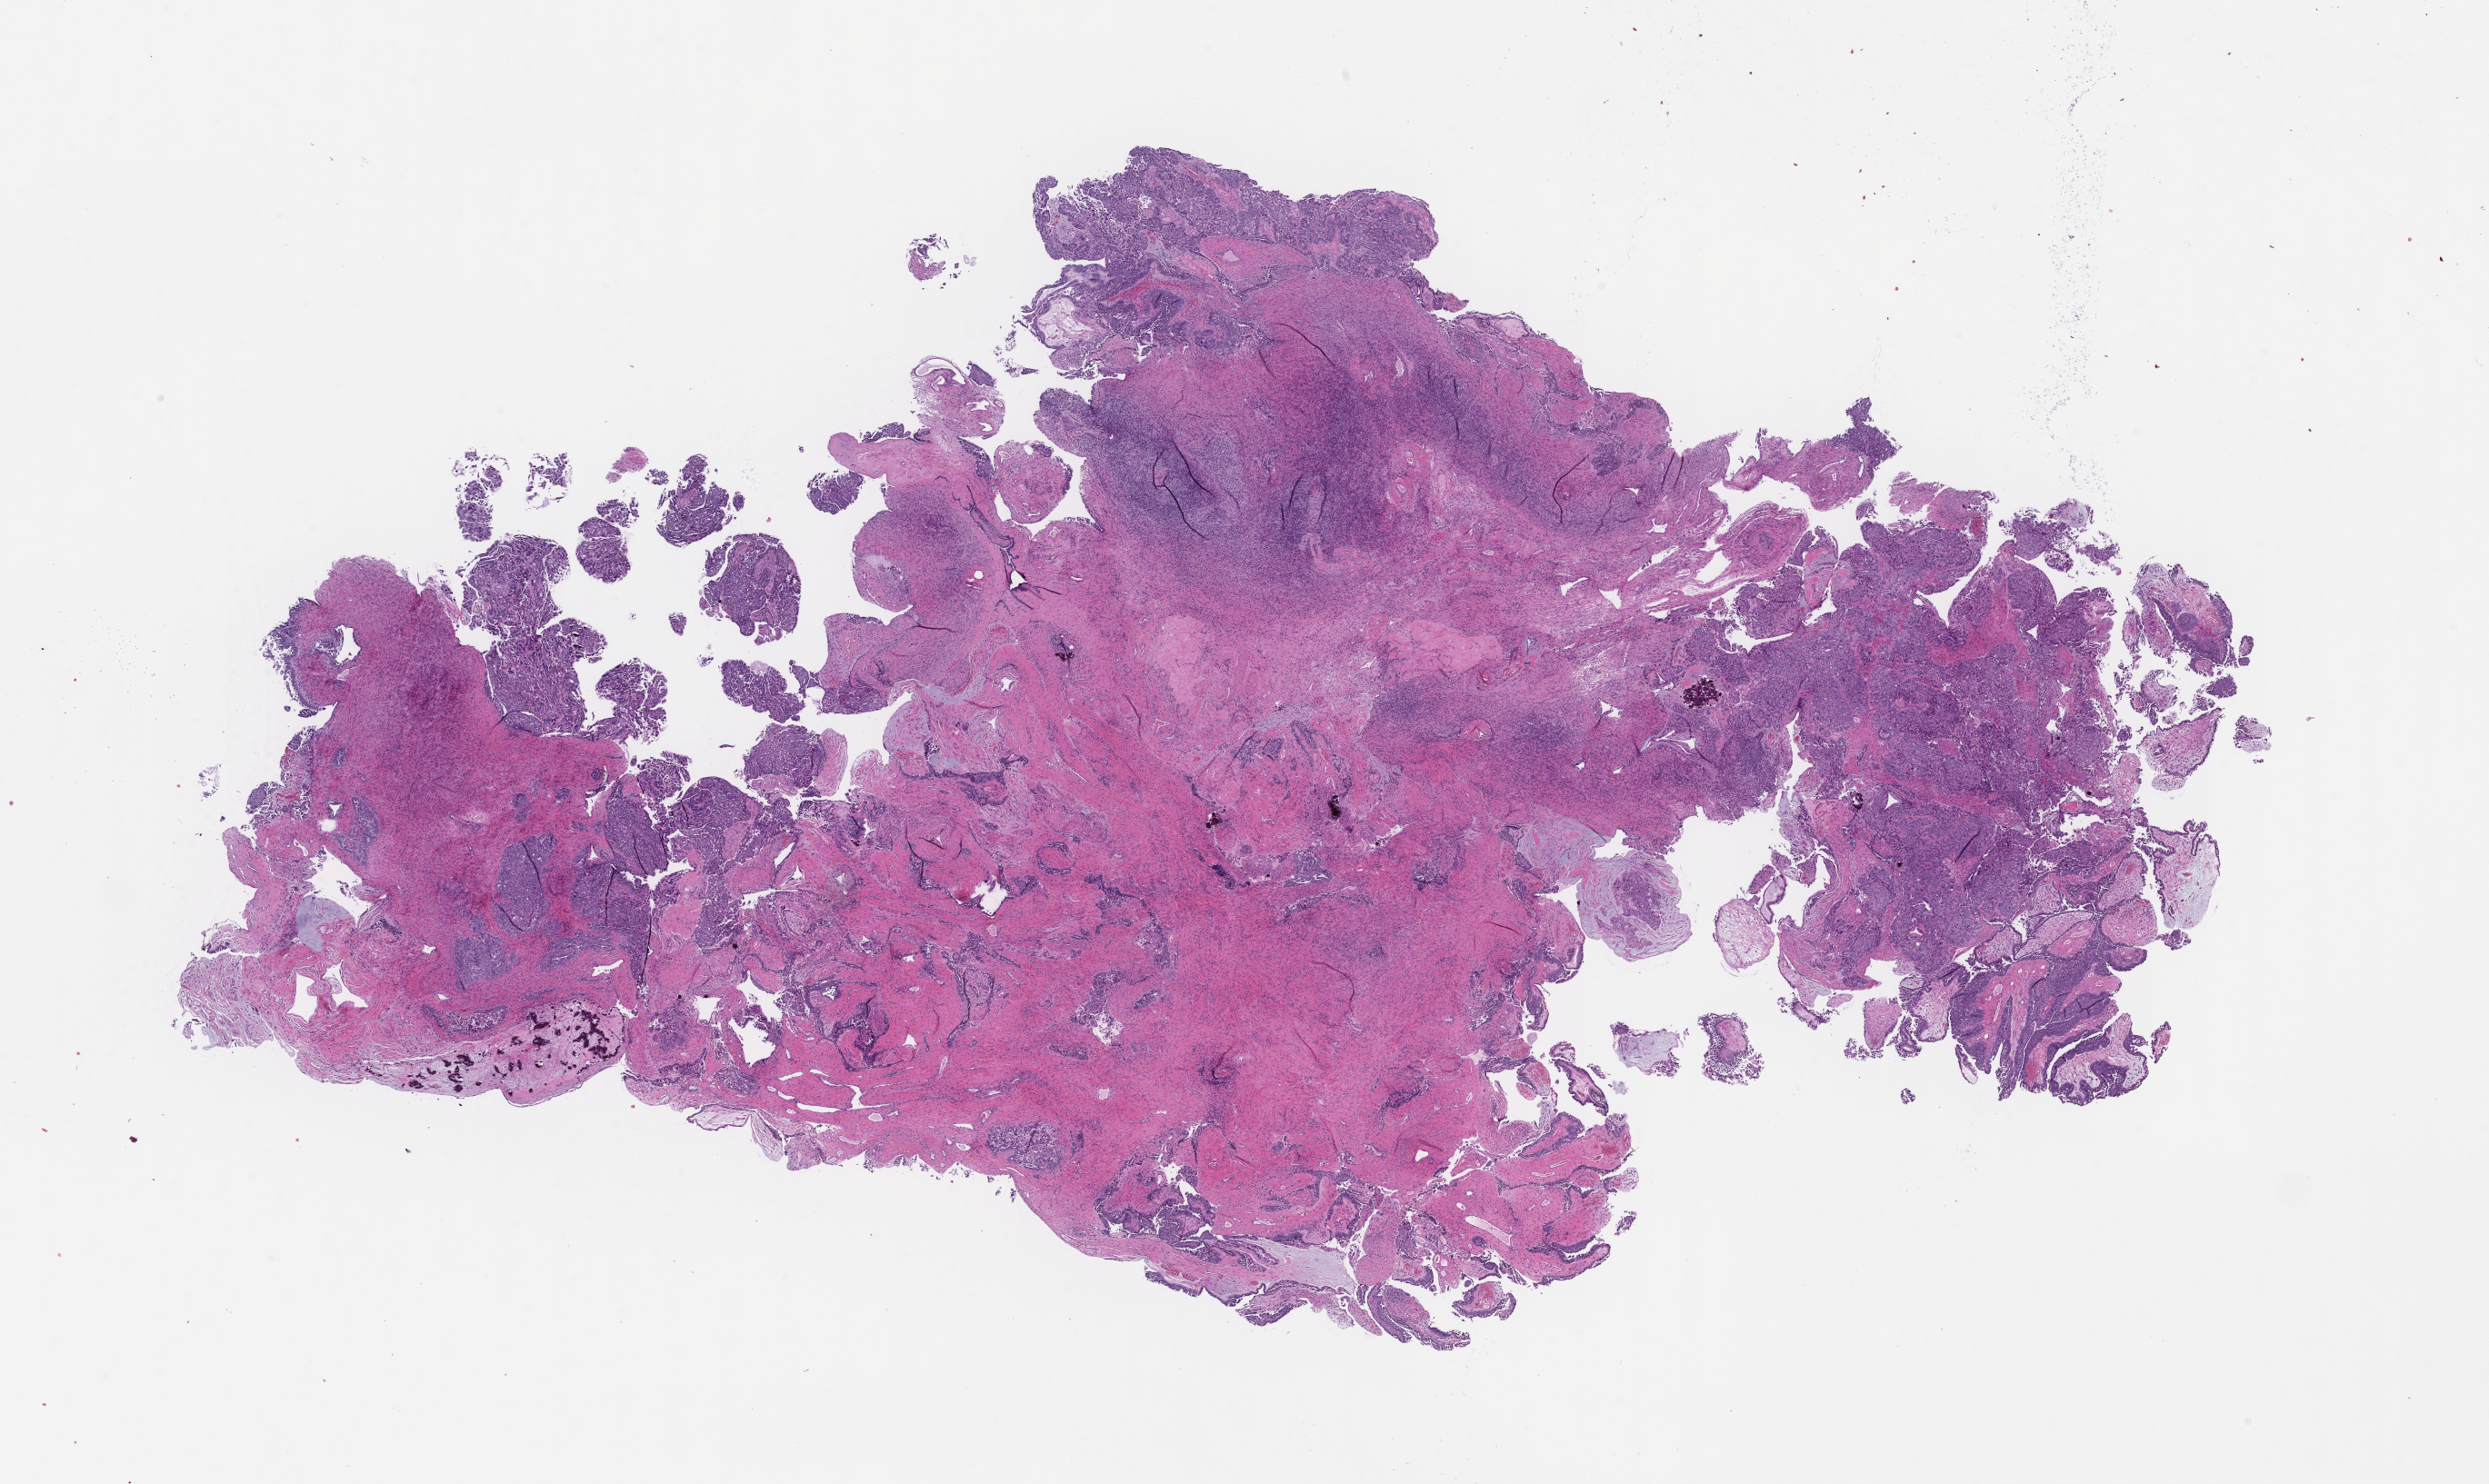
Digitized H&E-stained section, whole scanned area (about 22.1 x 13.2 mm) shown as a low-resolution overview. Formalin-fixed paraffin-embedded section. Site: ovary. Patient: female.
This section: primary tumour tissue. Diagnosis: Ovarian Carcinoma.